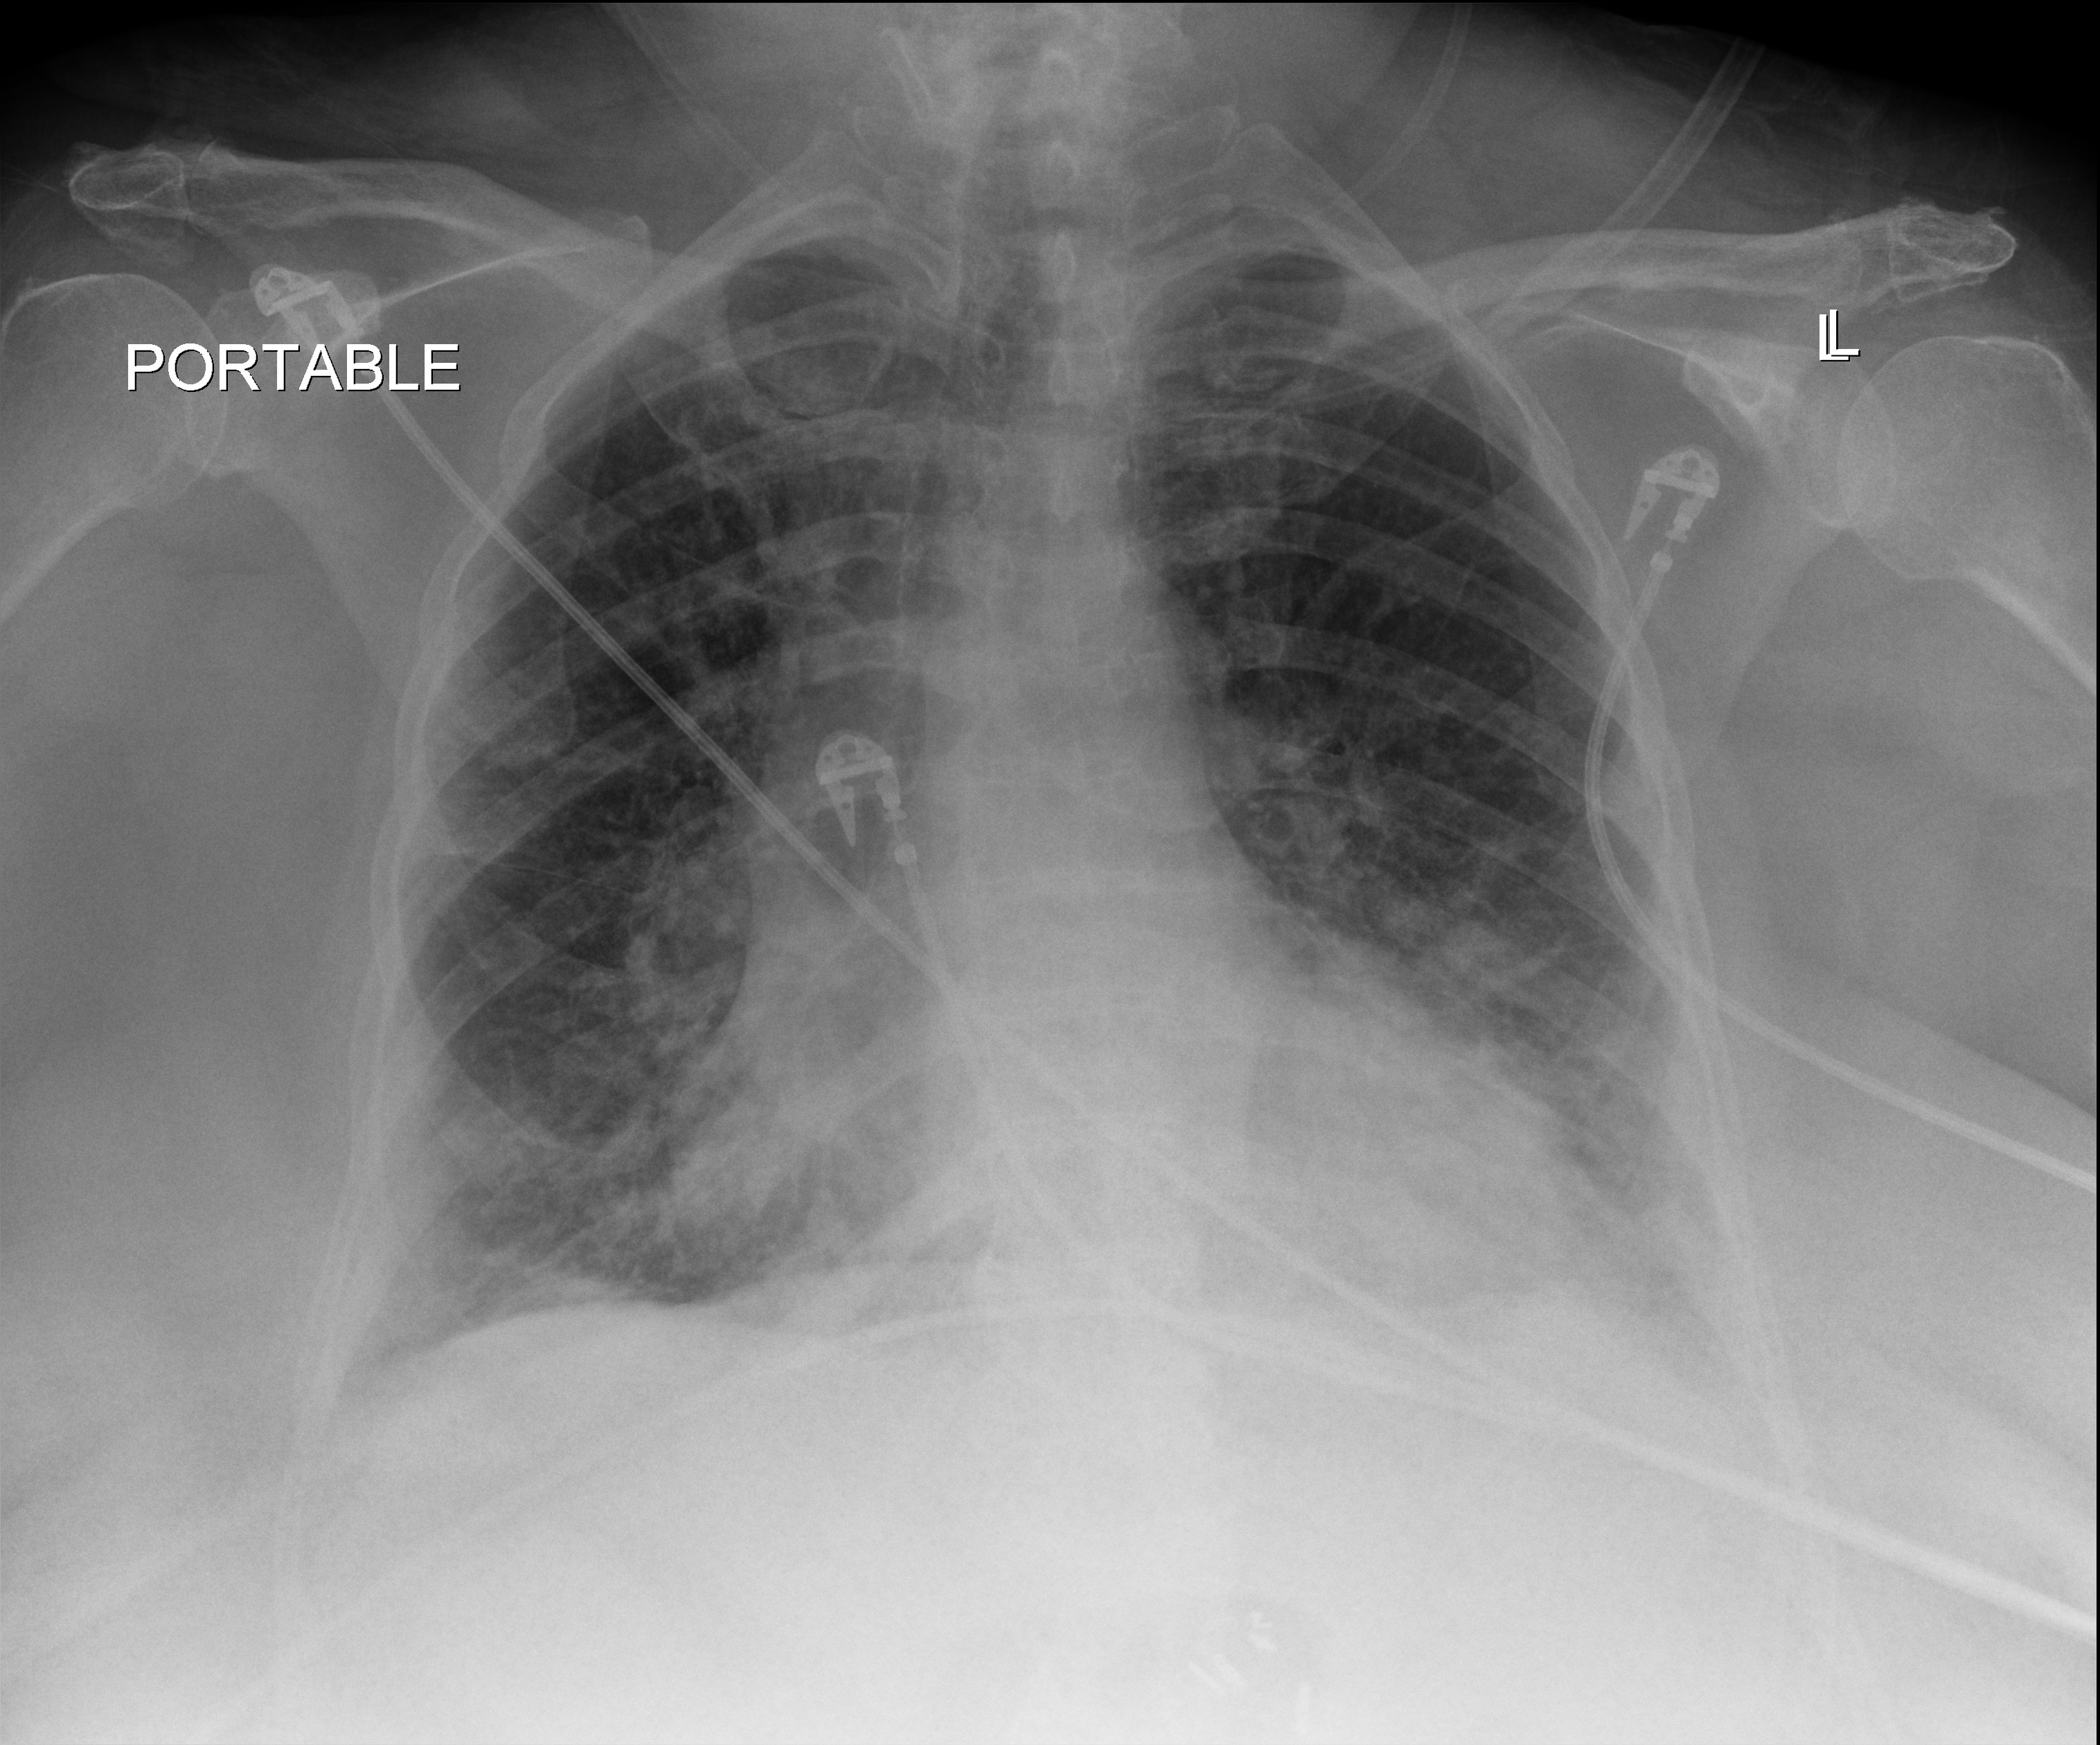
Chest X-ray (portable); anteroposterior (AP) projection. Female patient hospitalised with COVID-19, age 75–90 years.
Admission-level facts for this patient (not findings on this image; timing relative to this image not recorded): mechanically ventilated during this hospital stay: no; admitted to intensive care during this hospital stay: no.